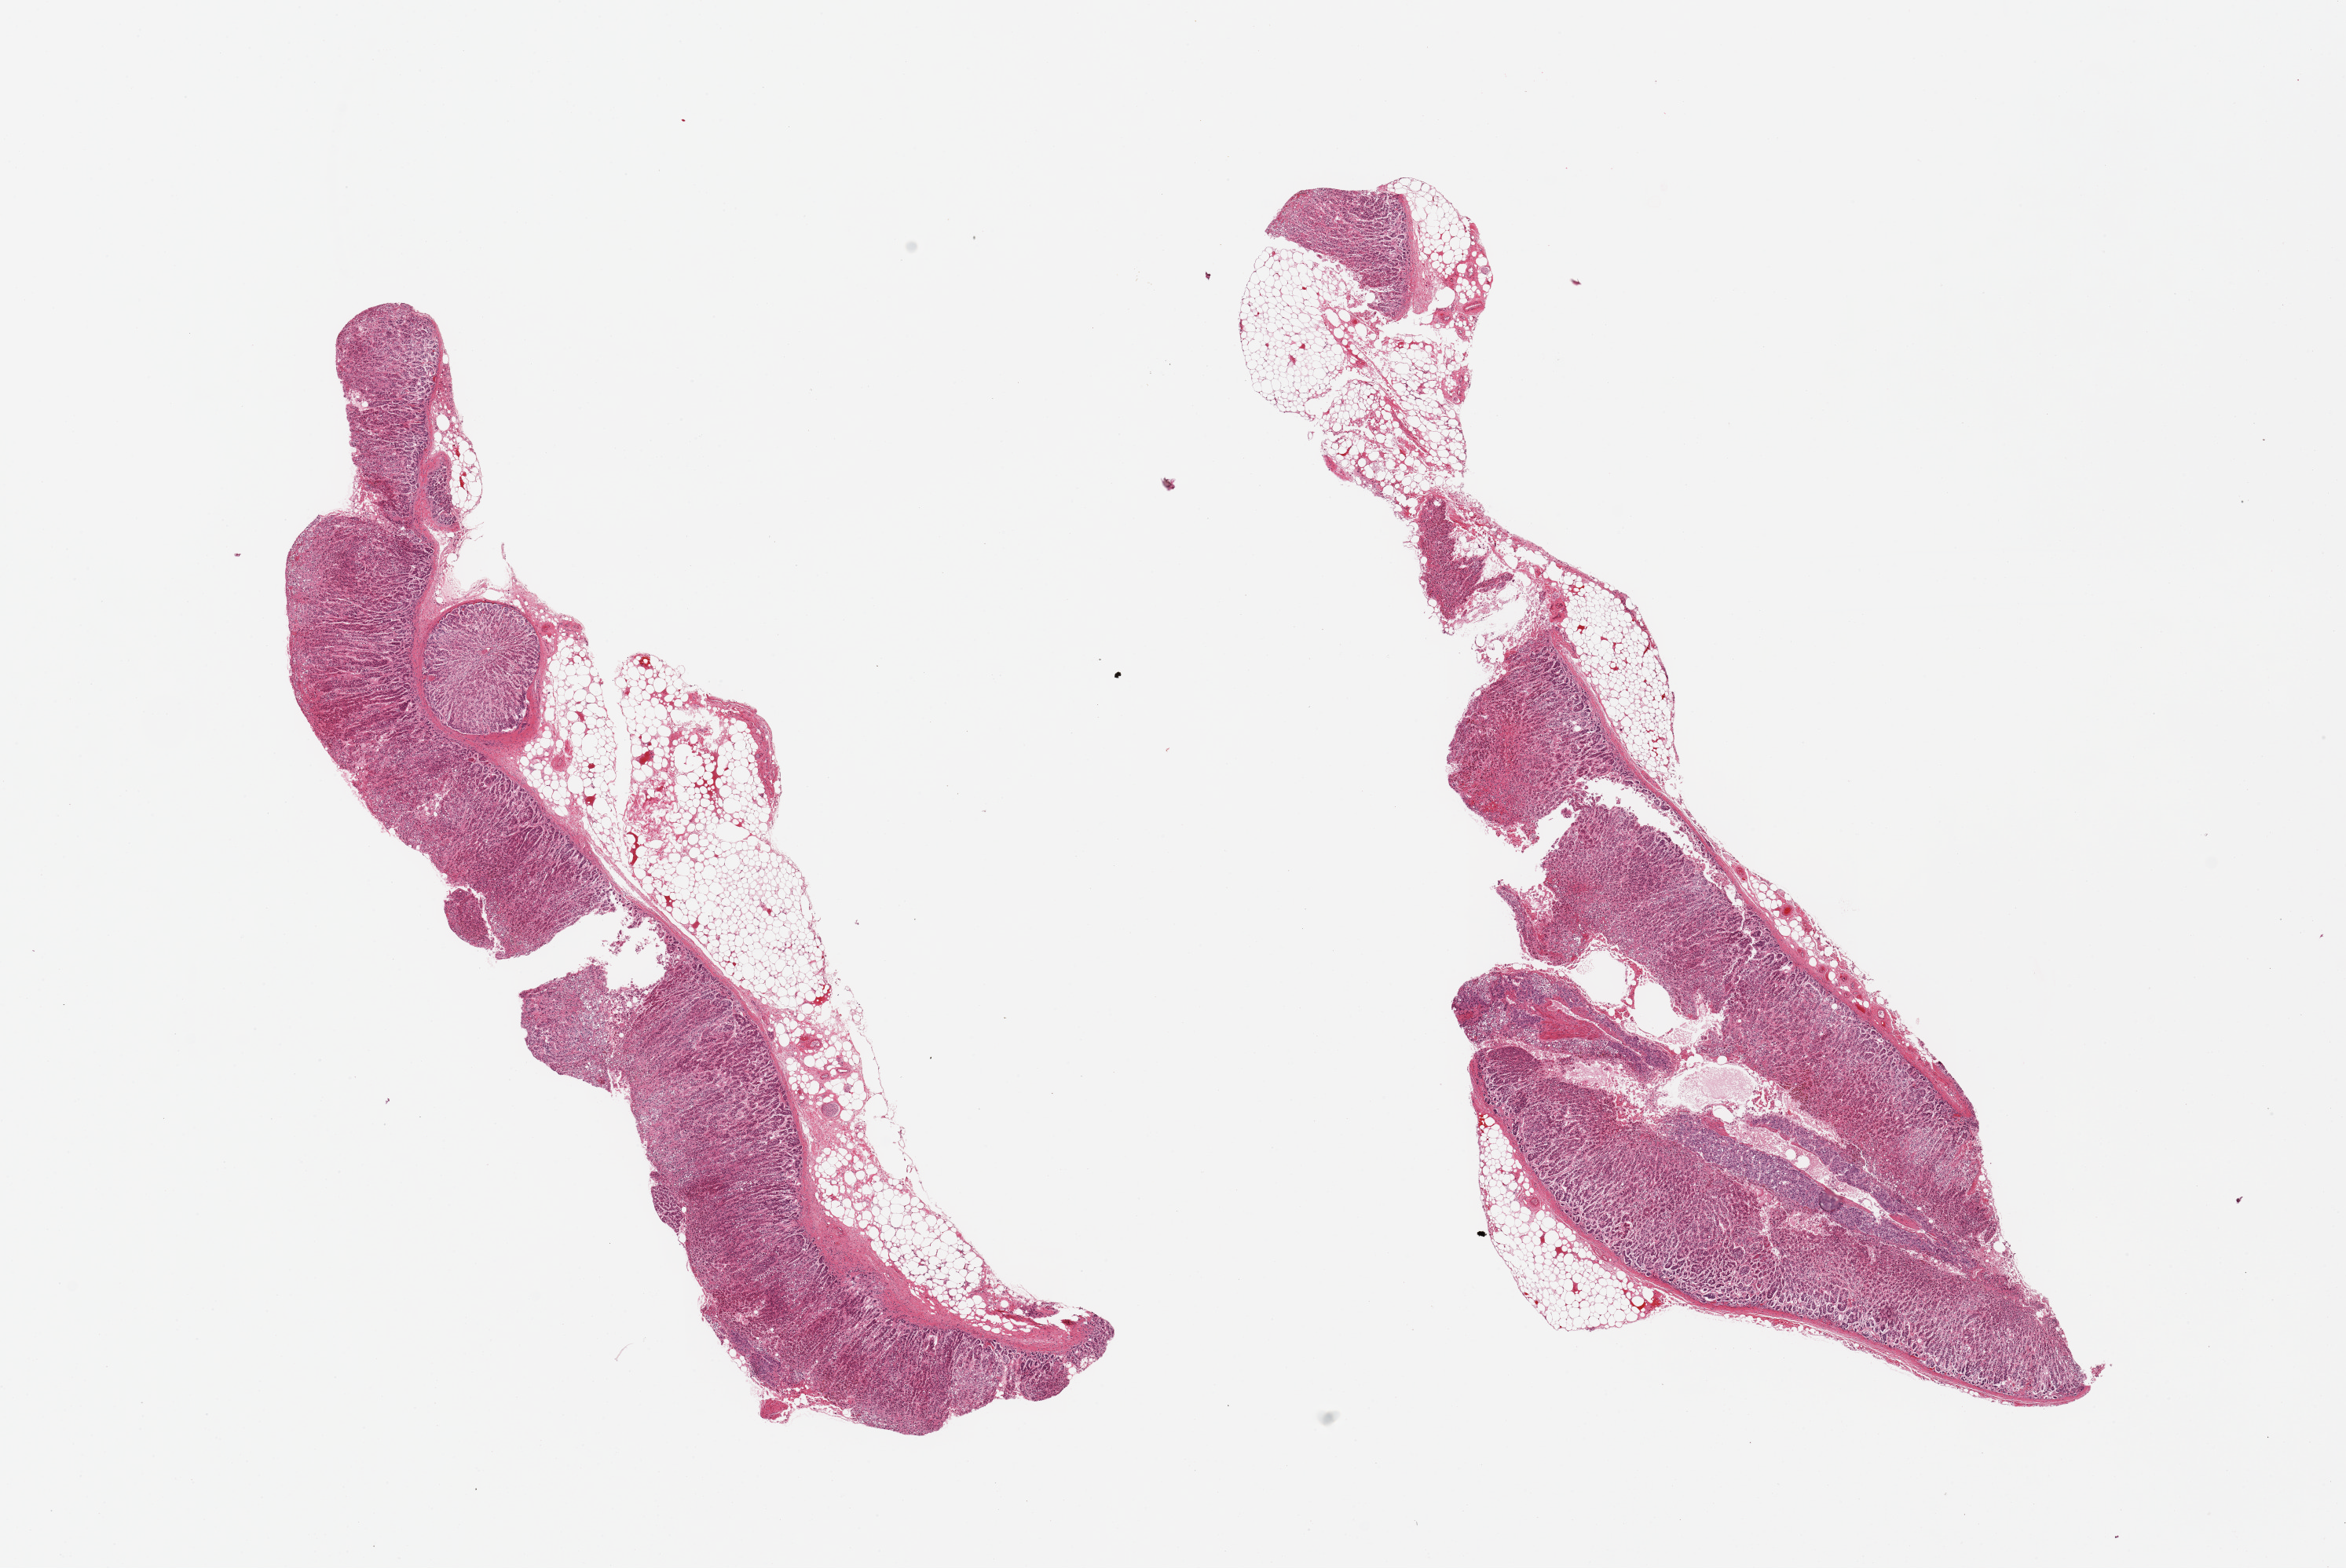
Haematoxylin and eosin whole-slide image, low-resolution overview of the scanned area, about 23.6 x 15.8 mm; PAXgene-fixed, paraffin-embedded tissue; target tissue: adrenal gland; donor tissue sample. Male donor.
Reviewer comment on this tissue sample: 2 pieces; 40% external fat.